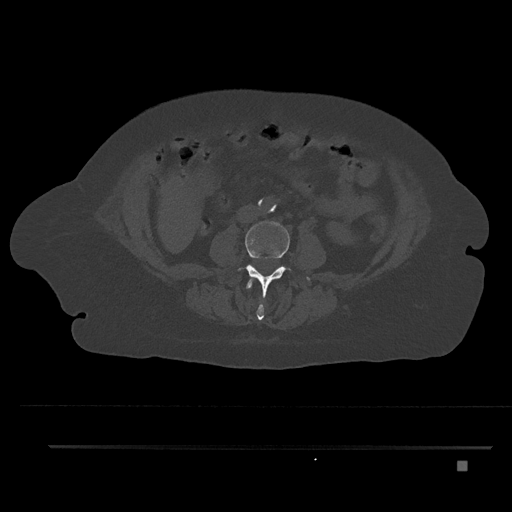
CT including the spine, one axial slice. Slice 126 of 797 in the series (ordered by position). Reconstruction kernel Br40s/3. Bone window (W 1800 / L 400 HU). 0.5 mm slice thickness. 512 × 512 image matrix, field of view 437 × 437 mm. Patient: female, 76 years. Case-level facts recorded for this patient, not image findings: primary cancer: lung.
Structures marked on this image (semi-automatically segmented with operator editing):
- L2 vertebra: bounding box [x1, y1, x2, y2] px = [246, 278, 264, 321]
- L3 vertebra: [236, 221, 311, 298]